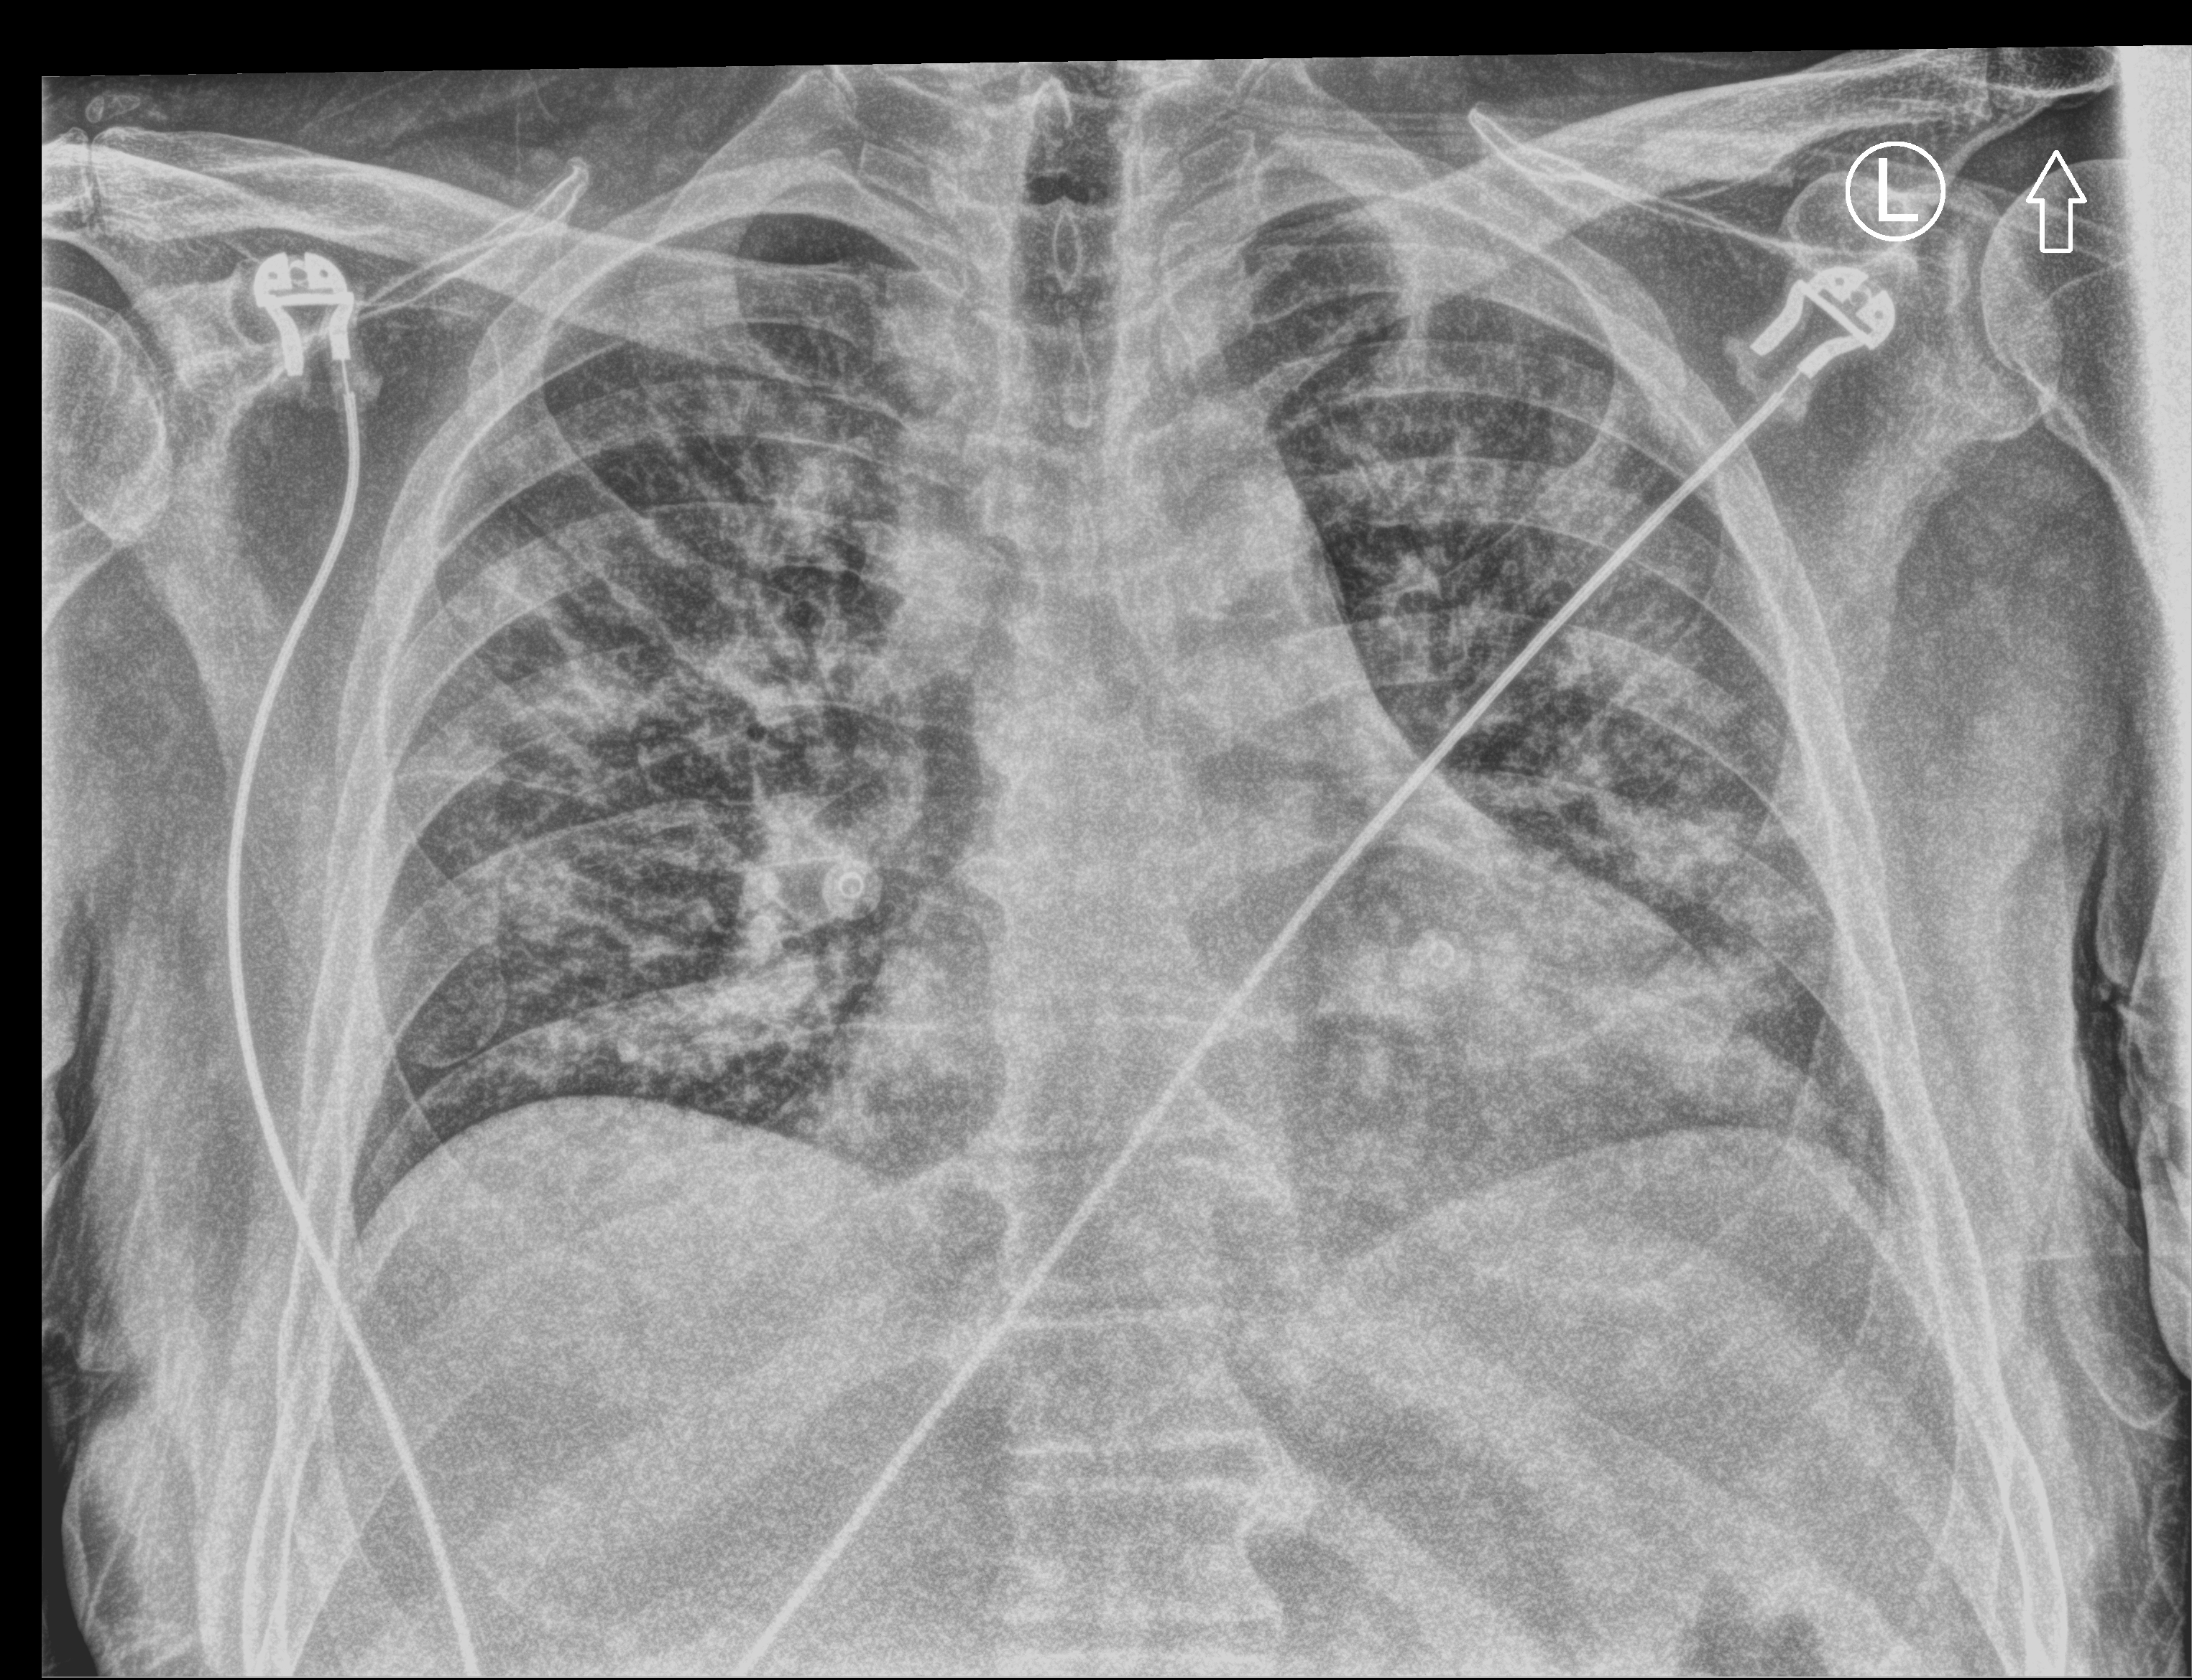
Portable chest radiograph; anteroposterior (AP) projection. Patient hospitalised with COVID-19; male, aged 60–74 years.
Admission-level facts for this patient (not findings on this image; timing relative to this image not recorded):
- admitted to intensive care during this hospital stay: yes